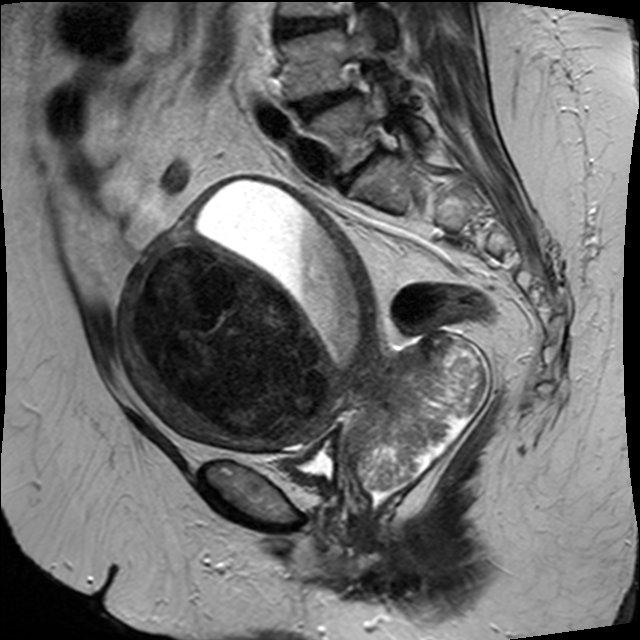
Pelvic MRI for cervical cancer, one sagittal slice; T2-weighted; 1.5 T; TE 89 ms, TR 3320 ms; 640 × 640 image matrix, field of view 260 × 260 mm. Patient: female, 50 years.
Annotated regions visible in this slice (outlined manually by an expert reader):
- uterus and cervix: bounding box [x1, y1, x2, y2] px = [120, 173, 486, 488]